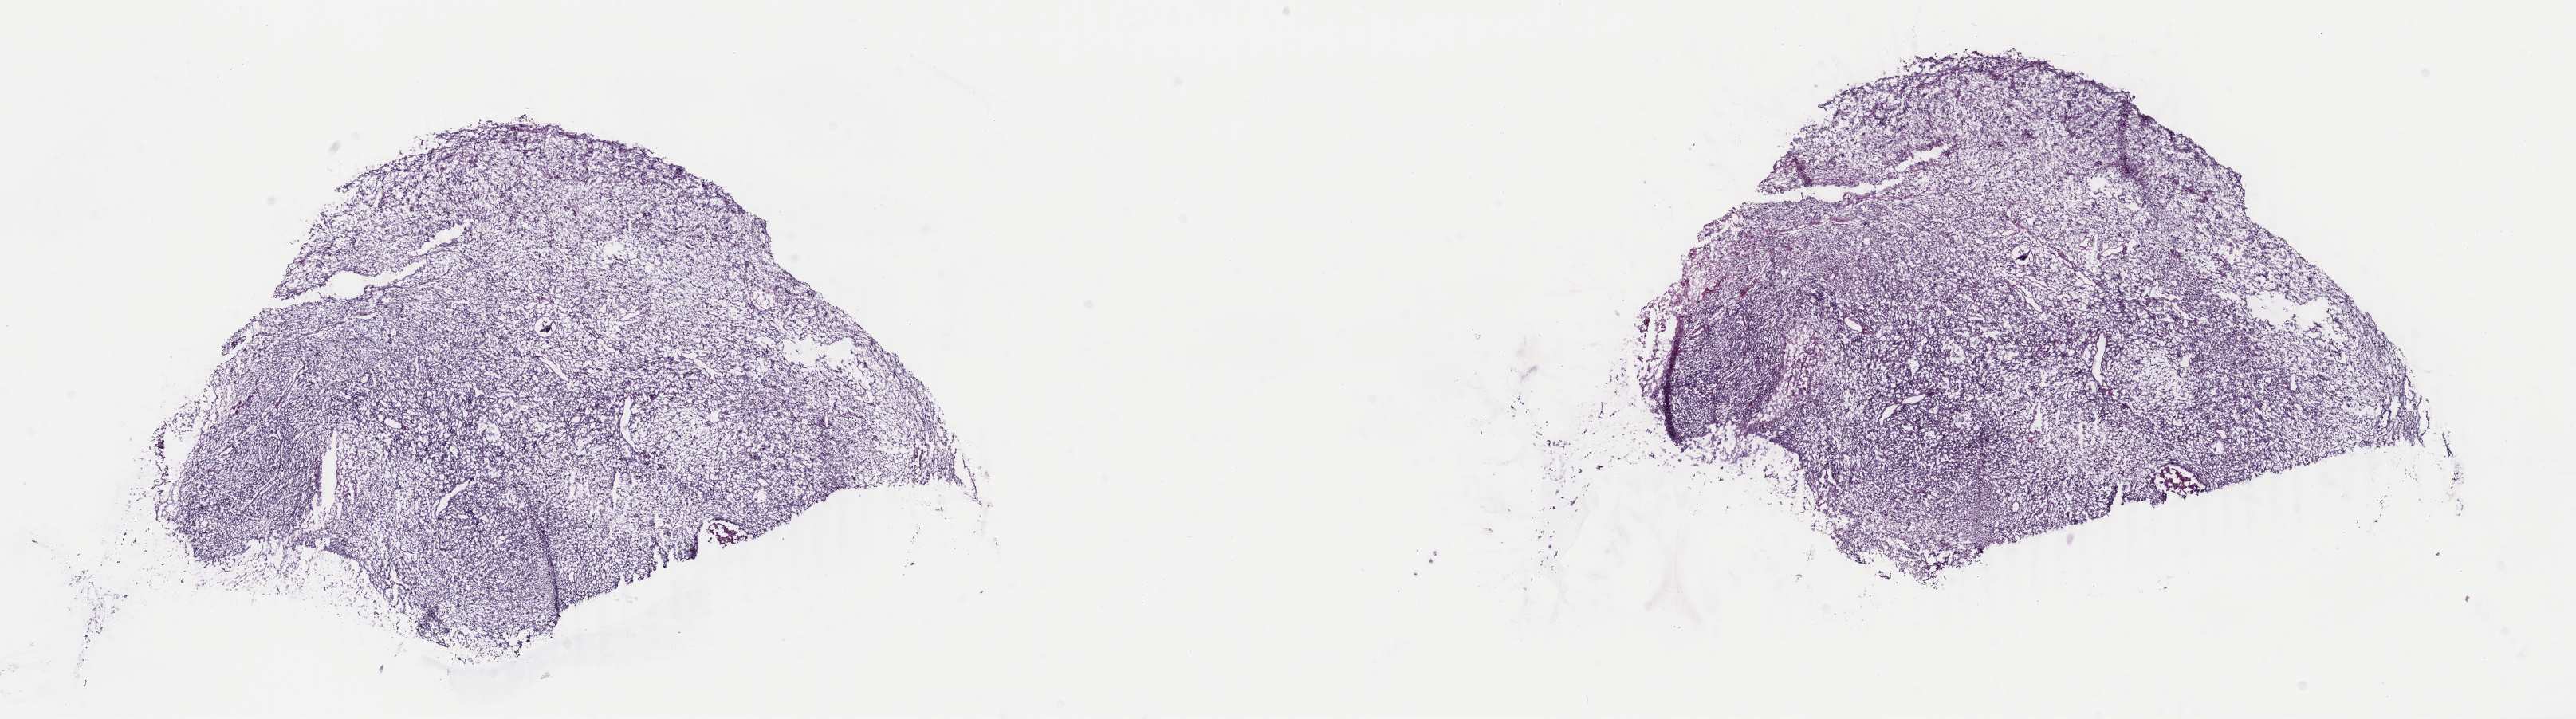
Digitized Hematoxylin and eosin (H&E) stained tissue section (whole slide) — shown as a low-resolution overview of the whole scanned area (about 25.7 x 7.2 mm, from a 40x scan). Frozen section from the top of the tissue portion. Sample: primary tumour, uterus. Female patient; age at initial diagnosis 68 years. Composition of this section per pathologist review: tumour cells 90%, tumour nuclei 90%, normal cells 0%, stromal cells 0%, necrosis 10%. Inflammatory infiltration, as recorded: lymphocyte infiltration 0%, monocyte infiltration 0%, neutrophil infiltration 0%.
Lymph nodes positive (case pathology): 0 of 9 examined. Diagnosis: Mullerian mixed tumor (endometrium). FIGO stage: IA.